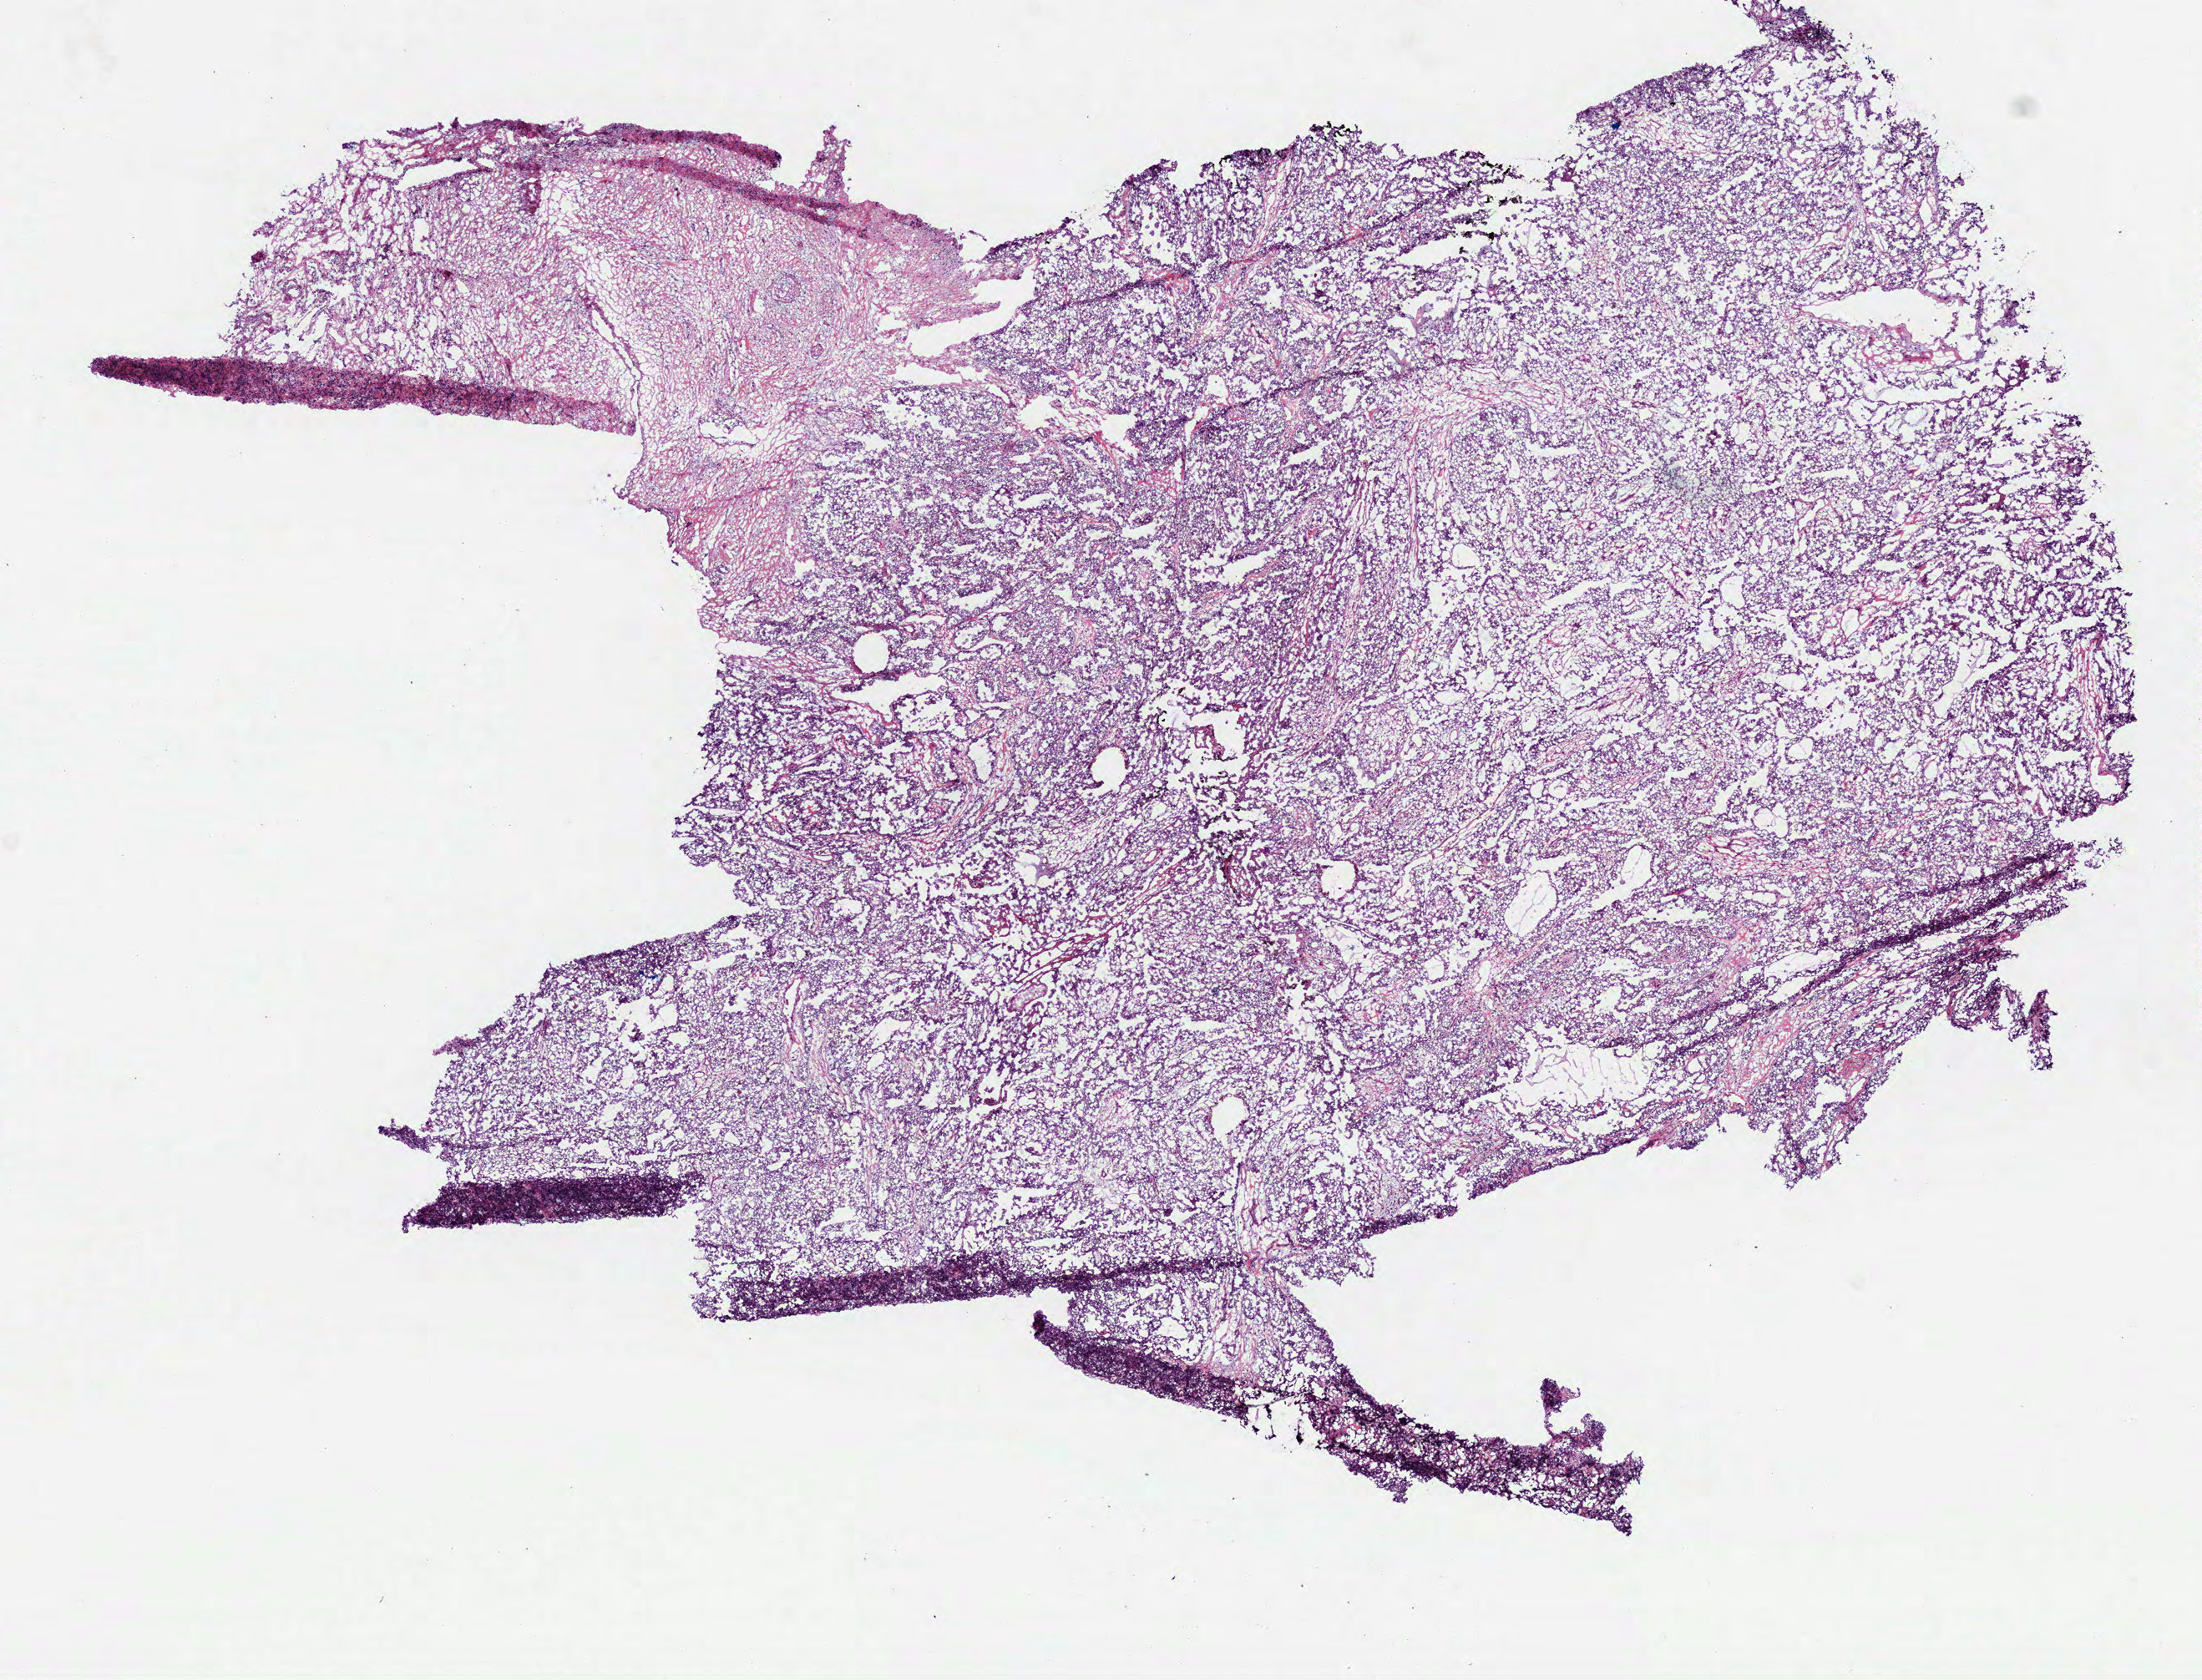
H&E whole-slide image, a low-resolution overview of the entire scanned area, about 10.6 x 8.1 mm (slide scanned at 40x), frozen section from the bottom of the tissue portion, kidney, primary tumour sample. Female patient; age at initial diagnosis 35 years. Slide review estimates, as recorded: tumour nuclei 75%, necrosis 0%.
AJCC pathologic stage: II (7th edition). TNM: T2b N0 MX. Laterality: left. Diagnosis: Papillary adenocarcinoma, NOS. Lymph nodes positive (case pathology): 0 of 2 examined.